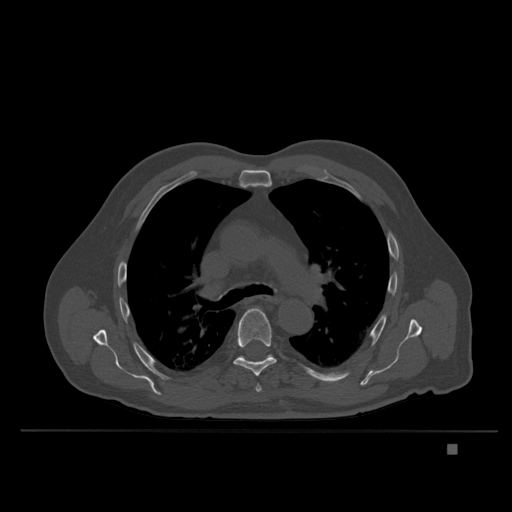
CT including the spine, one axial slice; position 259 of 435 along the scan axis; bone window (W 1800 / L 400 HU); 1.5 mm slice thickness; 512 × 512 image matrix, field of view 434 × 434 mm. Male patient, age 73 years. Case-level facts recorded for this patient, not image findings: primary cancer: skin.
Annotated regions visible in this slice (semi-automatically segmented with operator editing):
- T5 vertebra: bounding box (x1, y1, x2, y2) in pixels: (255, 385, 262, 392)
- T6 vertebra: (234, 308, 277, 377)
- T7 vertebra: (238, 355, 272, 362)